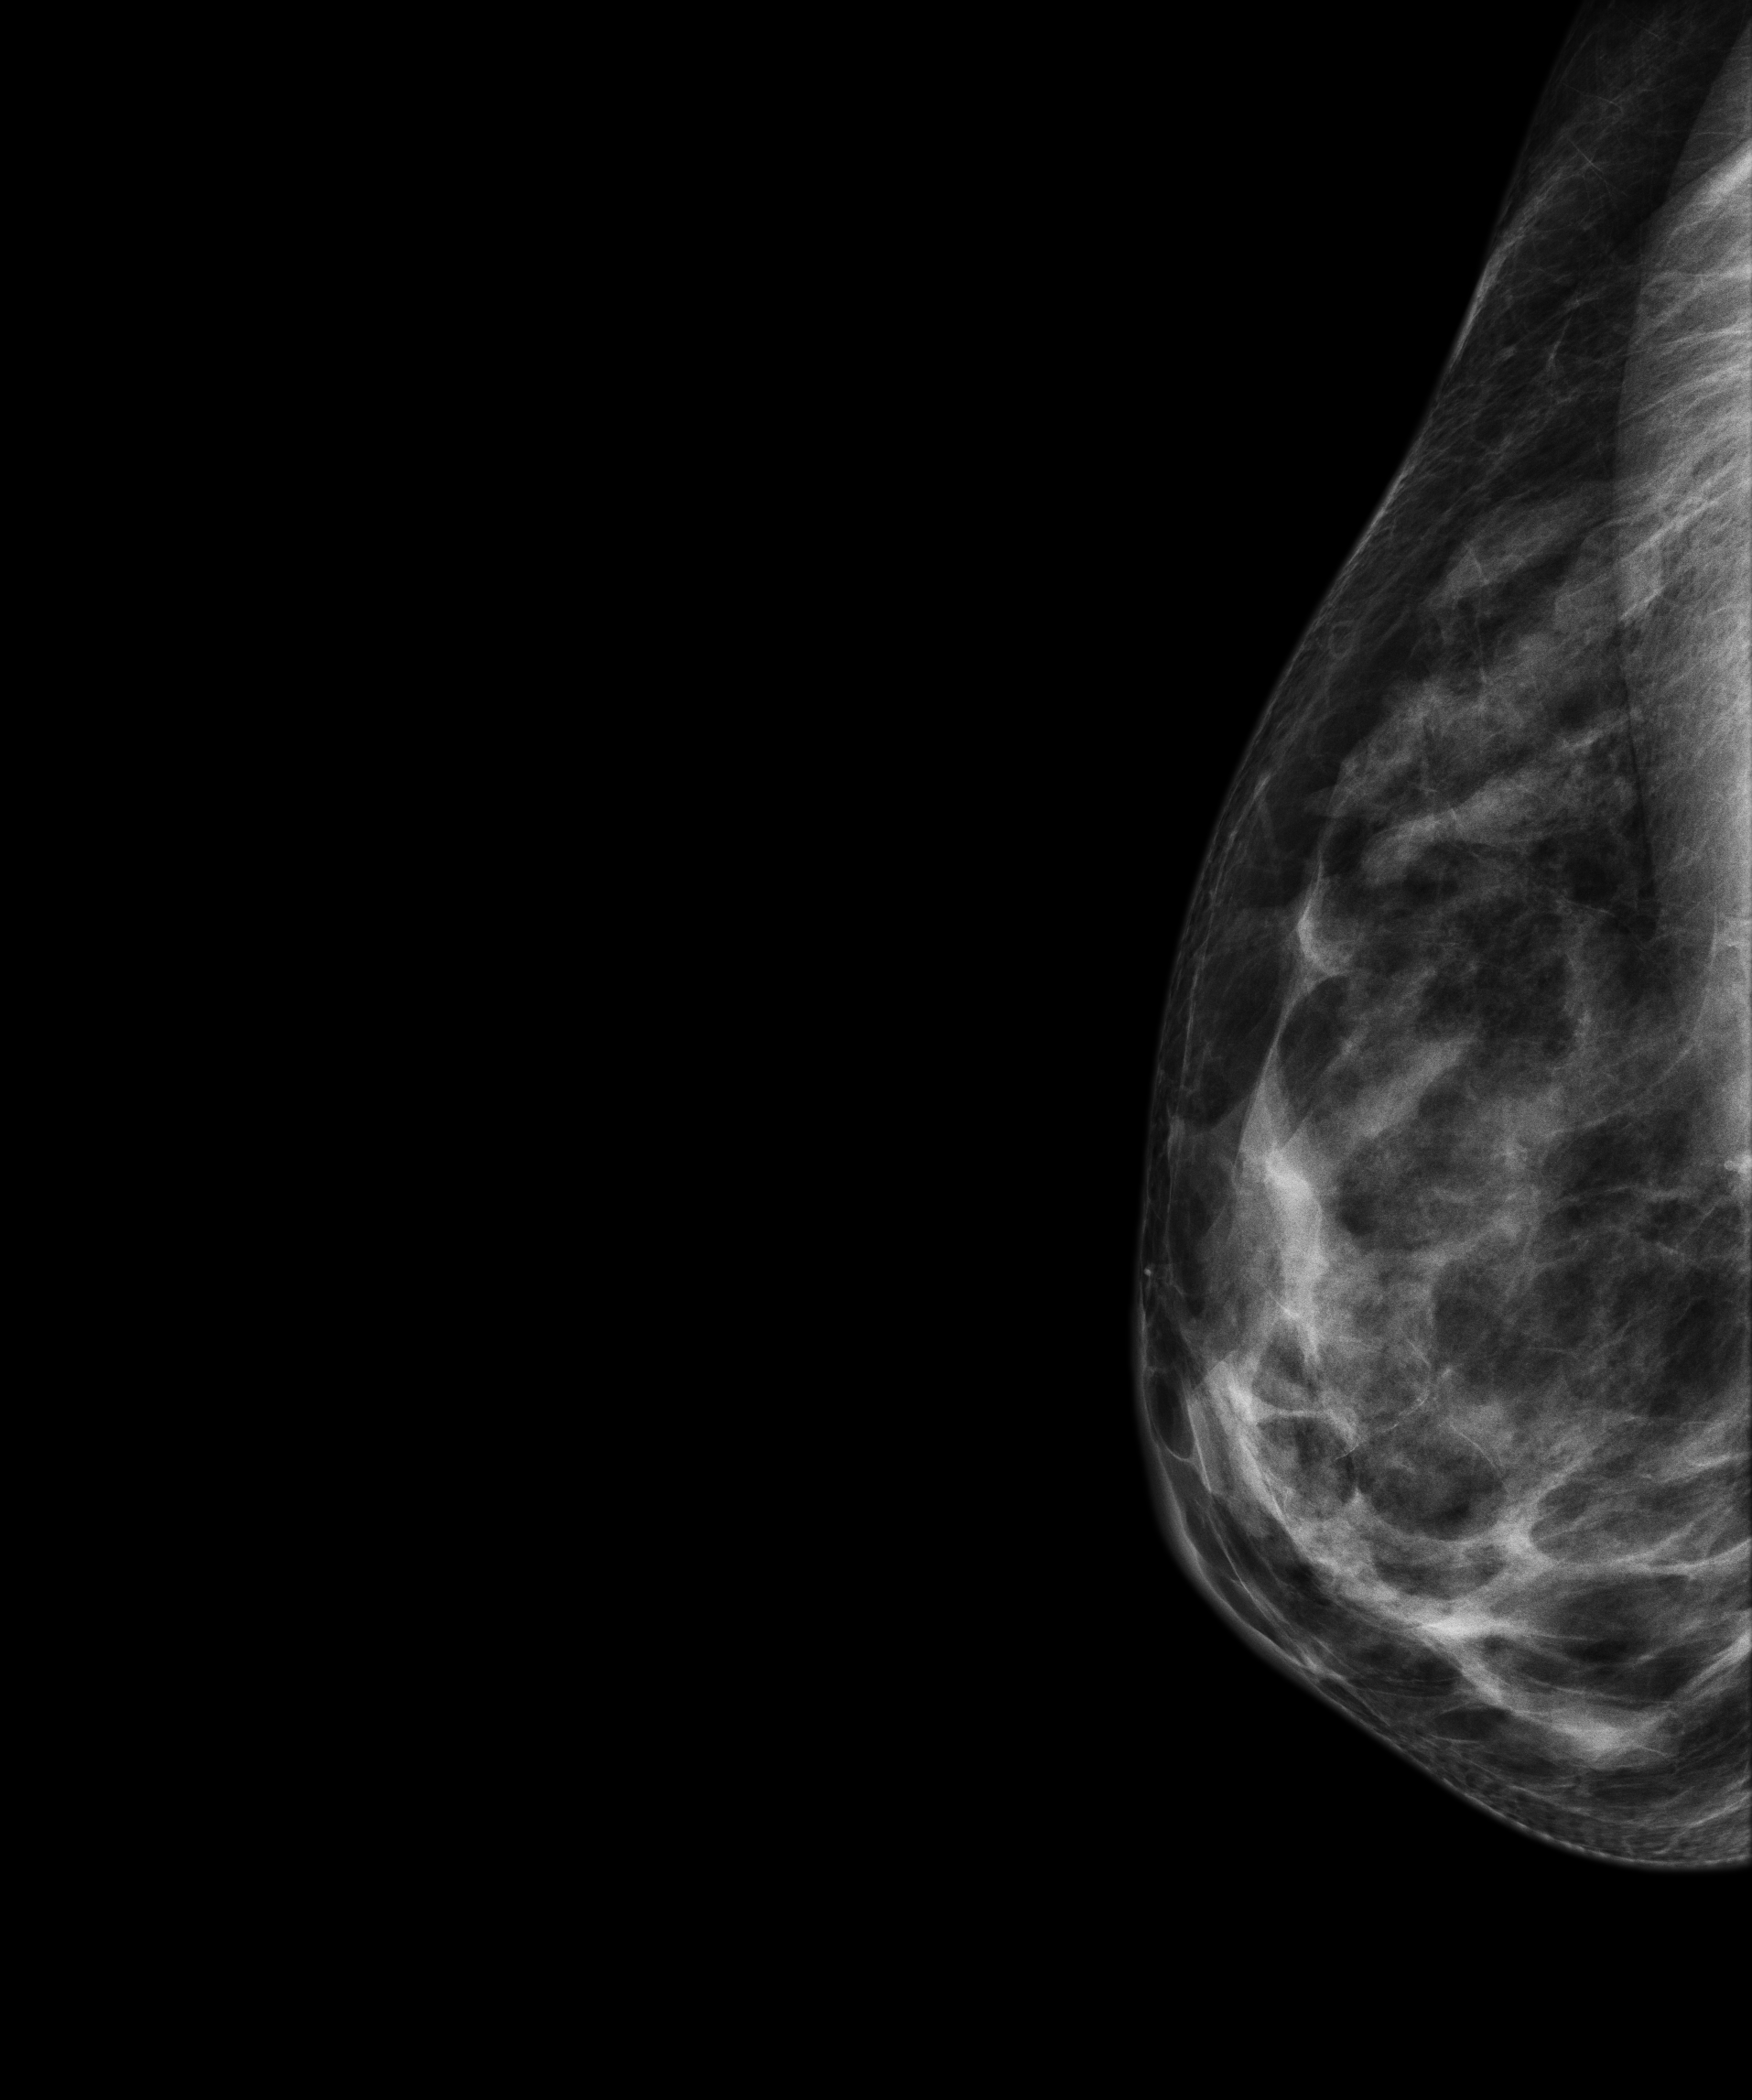
Annual screening mammography examination; compressed breast thickness 48 mm; system: Senographe Essential ADS_56.21.3. Female patient, age 67 years.
Image type: full-field digital mammogram. Breast: right. Projection: exaggerated CC view (lateral).